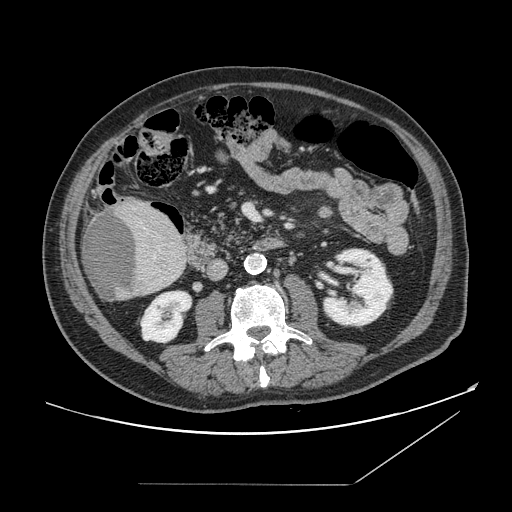
Contrast-enhanced abdominal CT, one axial slice; position 49 of 166 along the scan axis; intravenous contrast given; soft-tissue window (W 400 / L 40 HU); 2.5 mm slice thickness; 512 × 512 image matrix, field of view 416 × 416 mm. Male patient, age 80 years. From the clinical record (not read from this slice): diagnosis: colorectal cancer liver metastases, imaged before liver resection; multiple liver metastases: no; largest metastasis: 2.2 cm; disease in both lobes: no.
Annotated regions visible in this slice (manually delineated by an expert):
- liver: bounding box <82,199,187,301> (left, top, right, bottom; pixels)
- liver metastasis: <84,210,138,302>